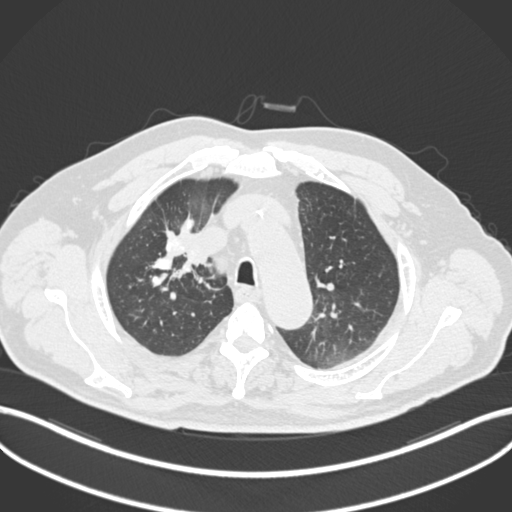
Chest CT, one axial slice. Slice 156 of 255 in the series (ordered by position). Reconstruction kernel B30f. 120 kVp. Lung window (W 1500 / L -600 HU). 1 mm slice thickness. 512 × 512 image matrix, field of view 400 × 400 mm. Patient: male, 60 years. From the clinical record (not read from this slice): clinical TNM (as recorded): T1b N1 M0.
Structures marked on this image (rectangle marked by the reading radiologist):
- lung tumour (recorded histology: squamous cell carcinoma): bounding box [x1, y1, x2, y2] px = [161, 230, 210, 272]